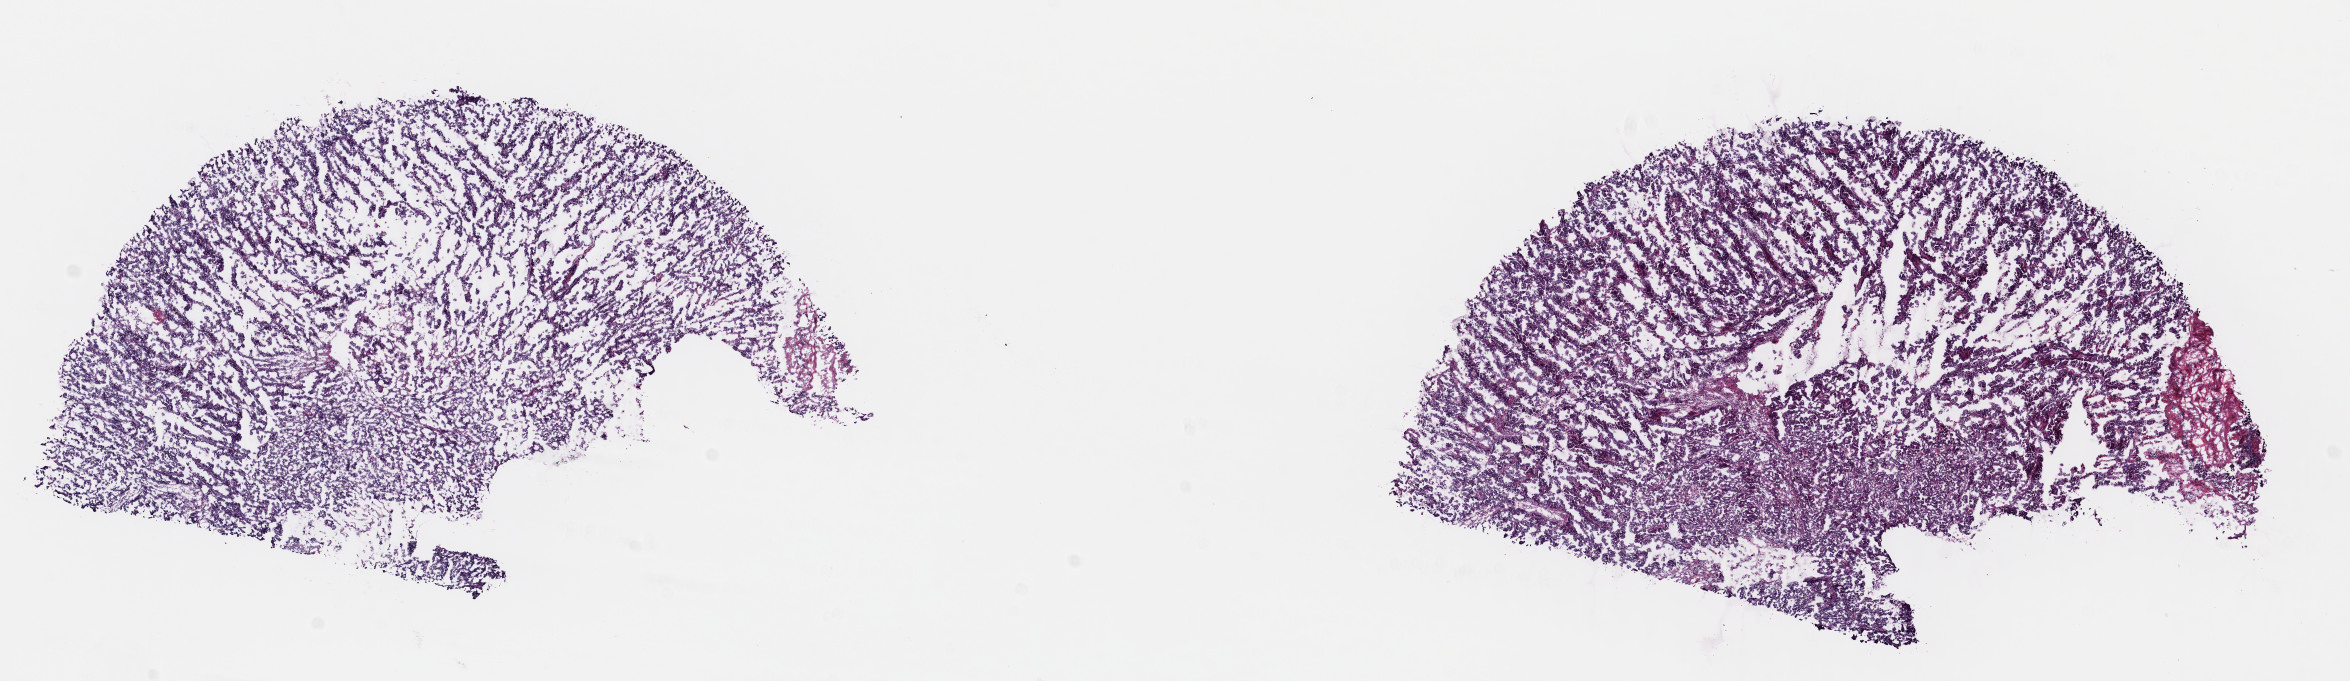
Digitized H&E-stained tissue section (whole slide) — a low-resolution overview of the entire scanned area, about 18.5 x 5.4 mm; frozen section from the top of the tissue portion; sample: primary tumour, uterus. Female, age 63 years at initial diagnosis. Histologic grade: G3 (poorly differentiated). Slide review estimates, as recorded: tumour cells 80%, tumour nuclei 80%, normal cells 0%, stromal cells 20%, necrosis 0%. Inflammatory infiltration, as recorded: lymphocyte infiltration 0%, monocyte infiltration 0%, neutrophil infiltration 0%.
FIGO stage: IIIC2. Lymph nodes positive (case pathology): 8 of 17 examined. Diagnosis: Serous cystadenocarcinoma, NOS (endometrium).